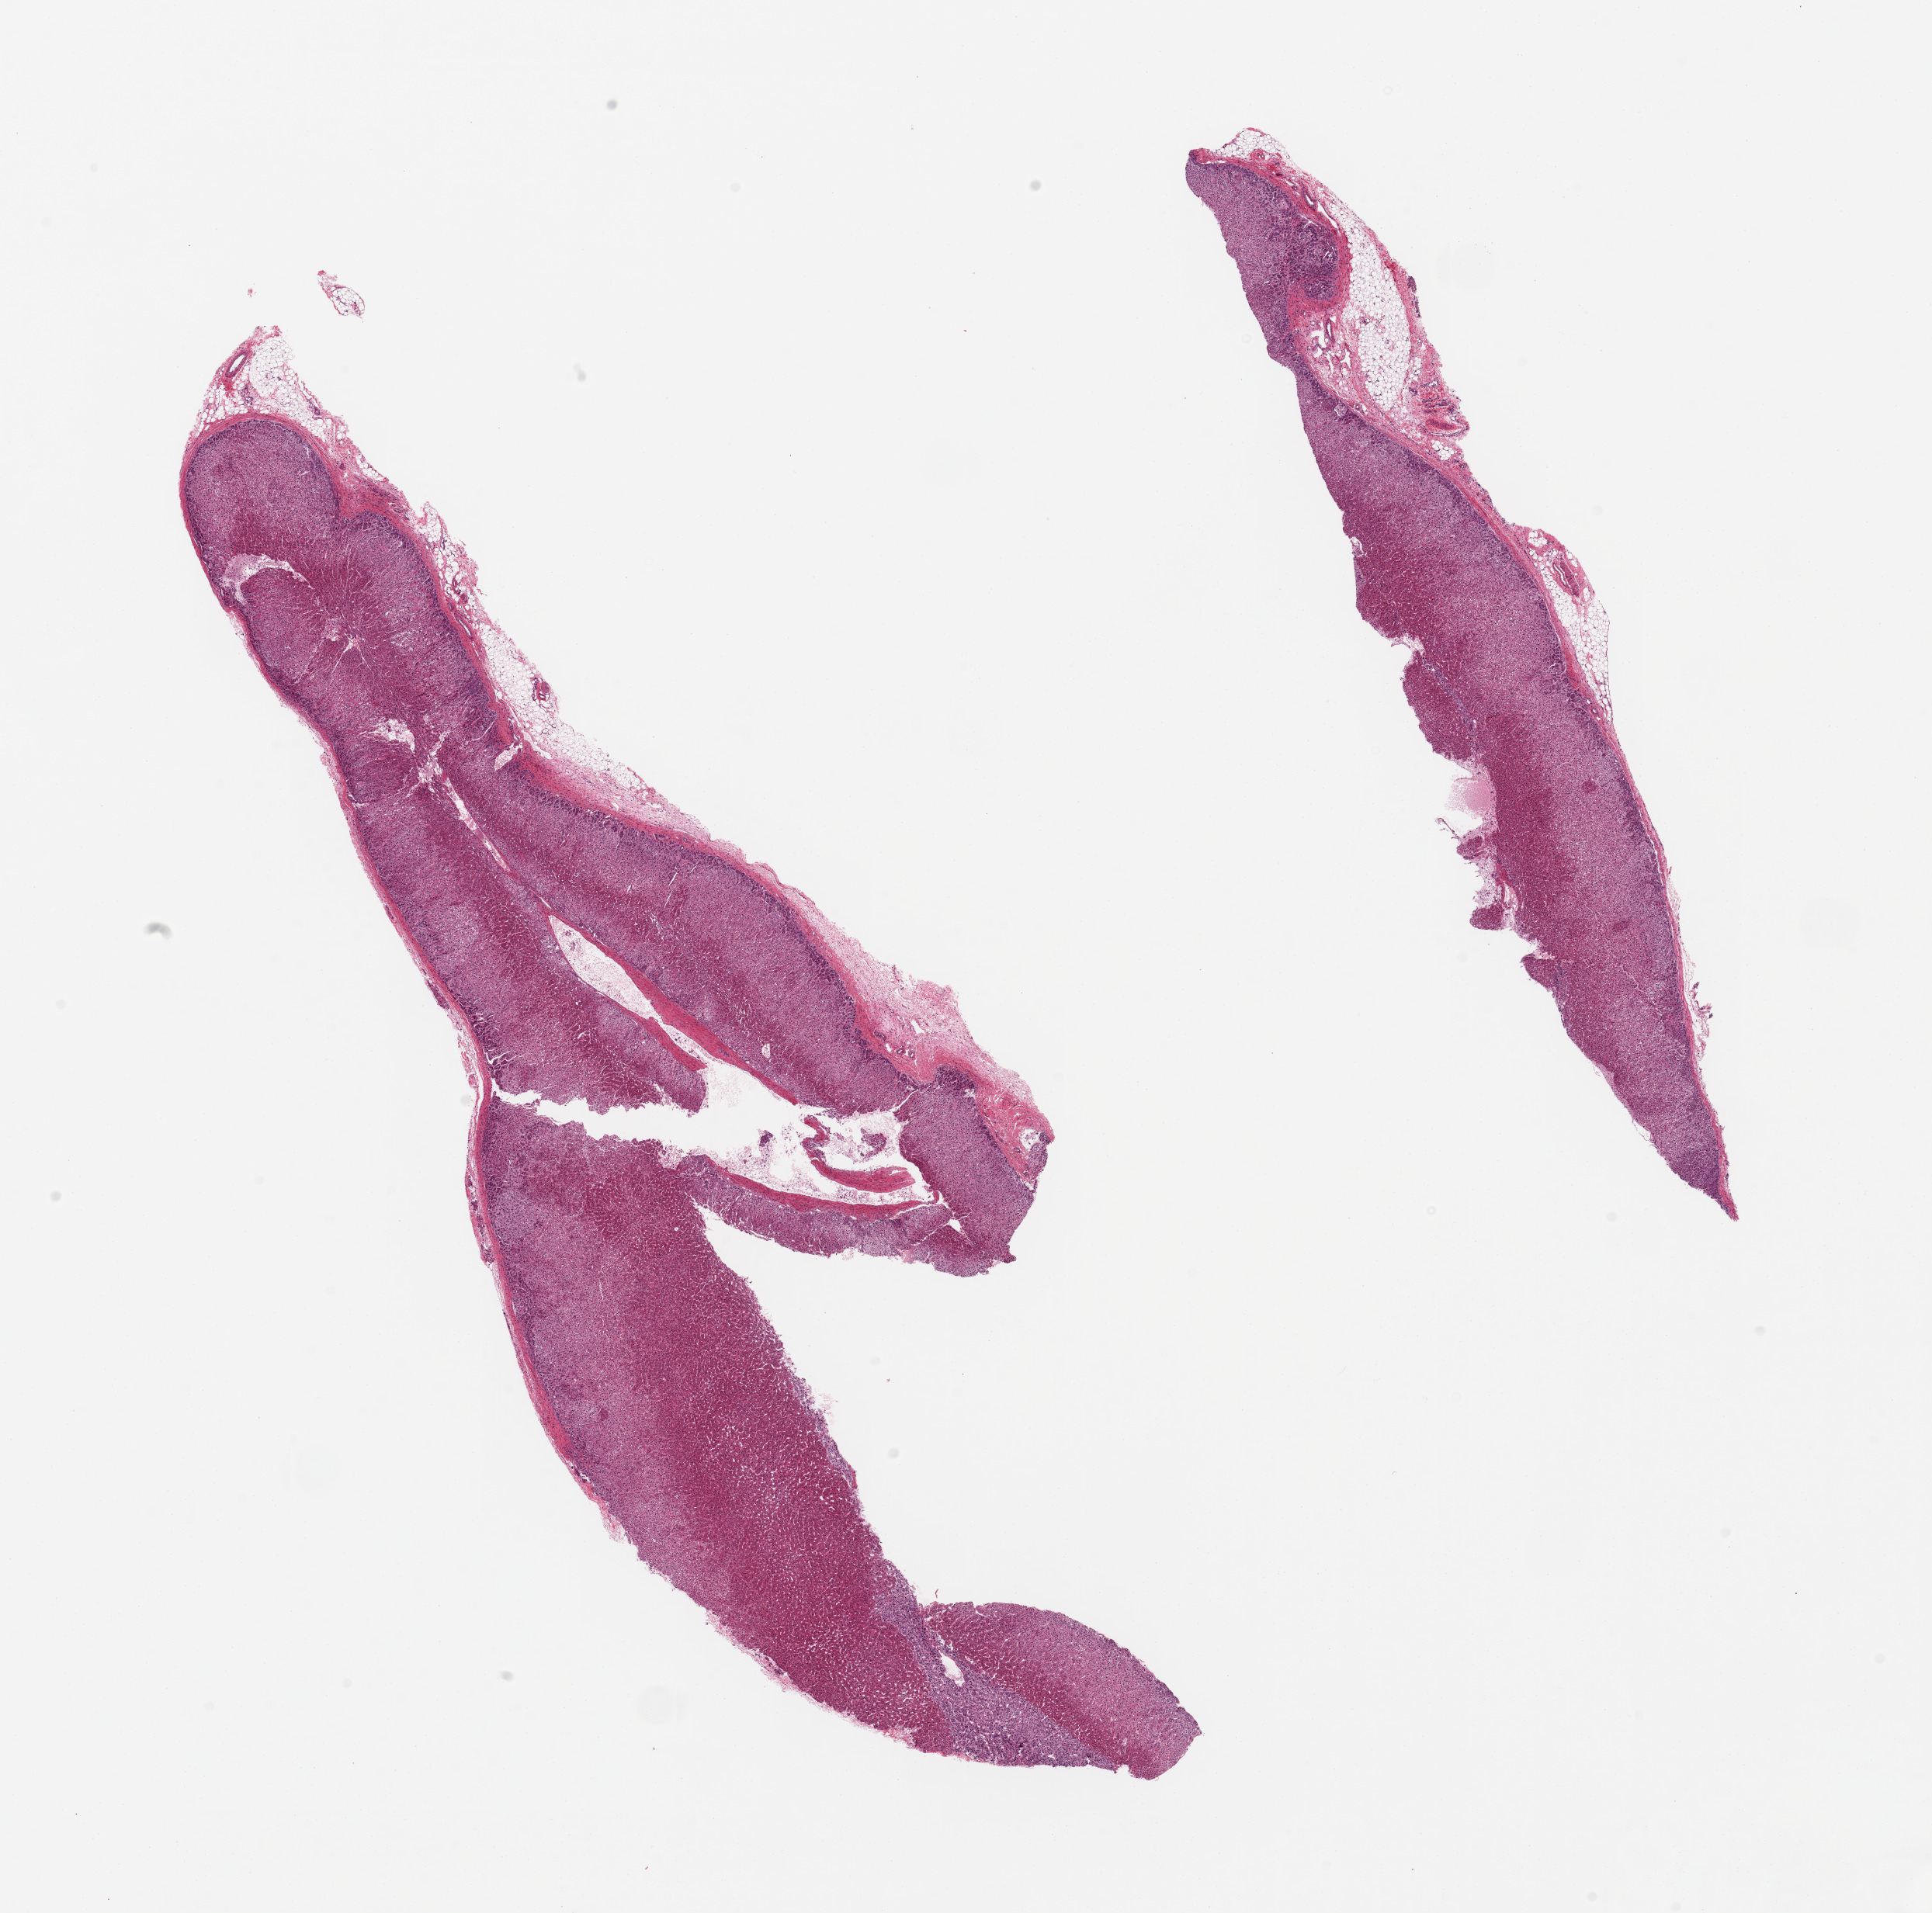
Whole-slide image, H&E stain, whole scanned area (about 19.7 x 19.5 mm) shown as a low-resolution overview, PAXgene-fixed paraffin-embedded (PFPE) section, sampled site (target tissue): adrenal gland, donor tissue sample. Female donor.
Reviewer comment on this tissue sample: 2 pieces; <5% fat; well dissected.